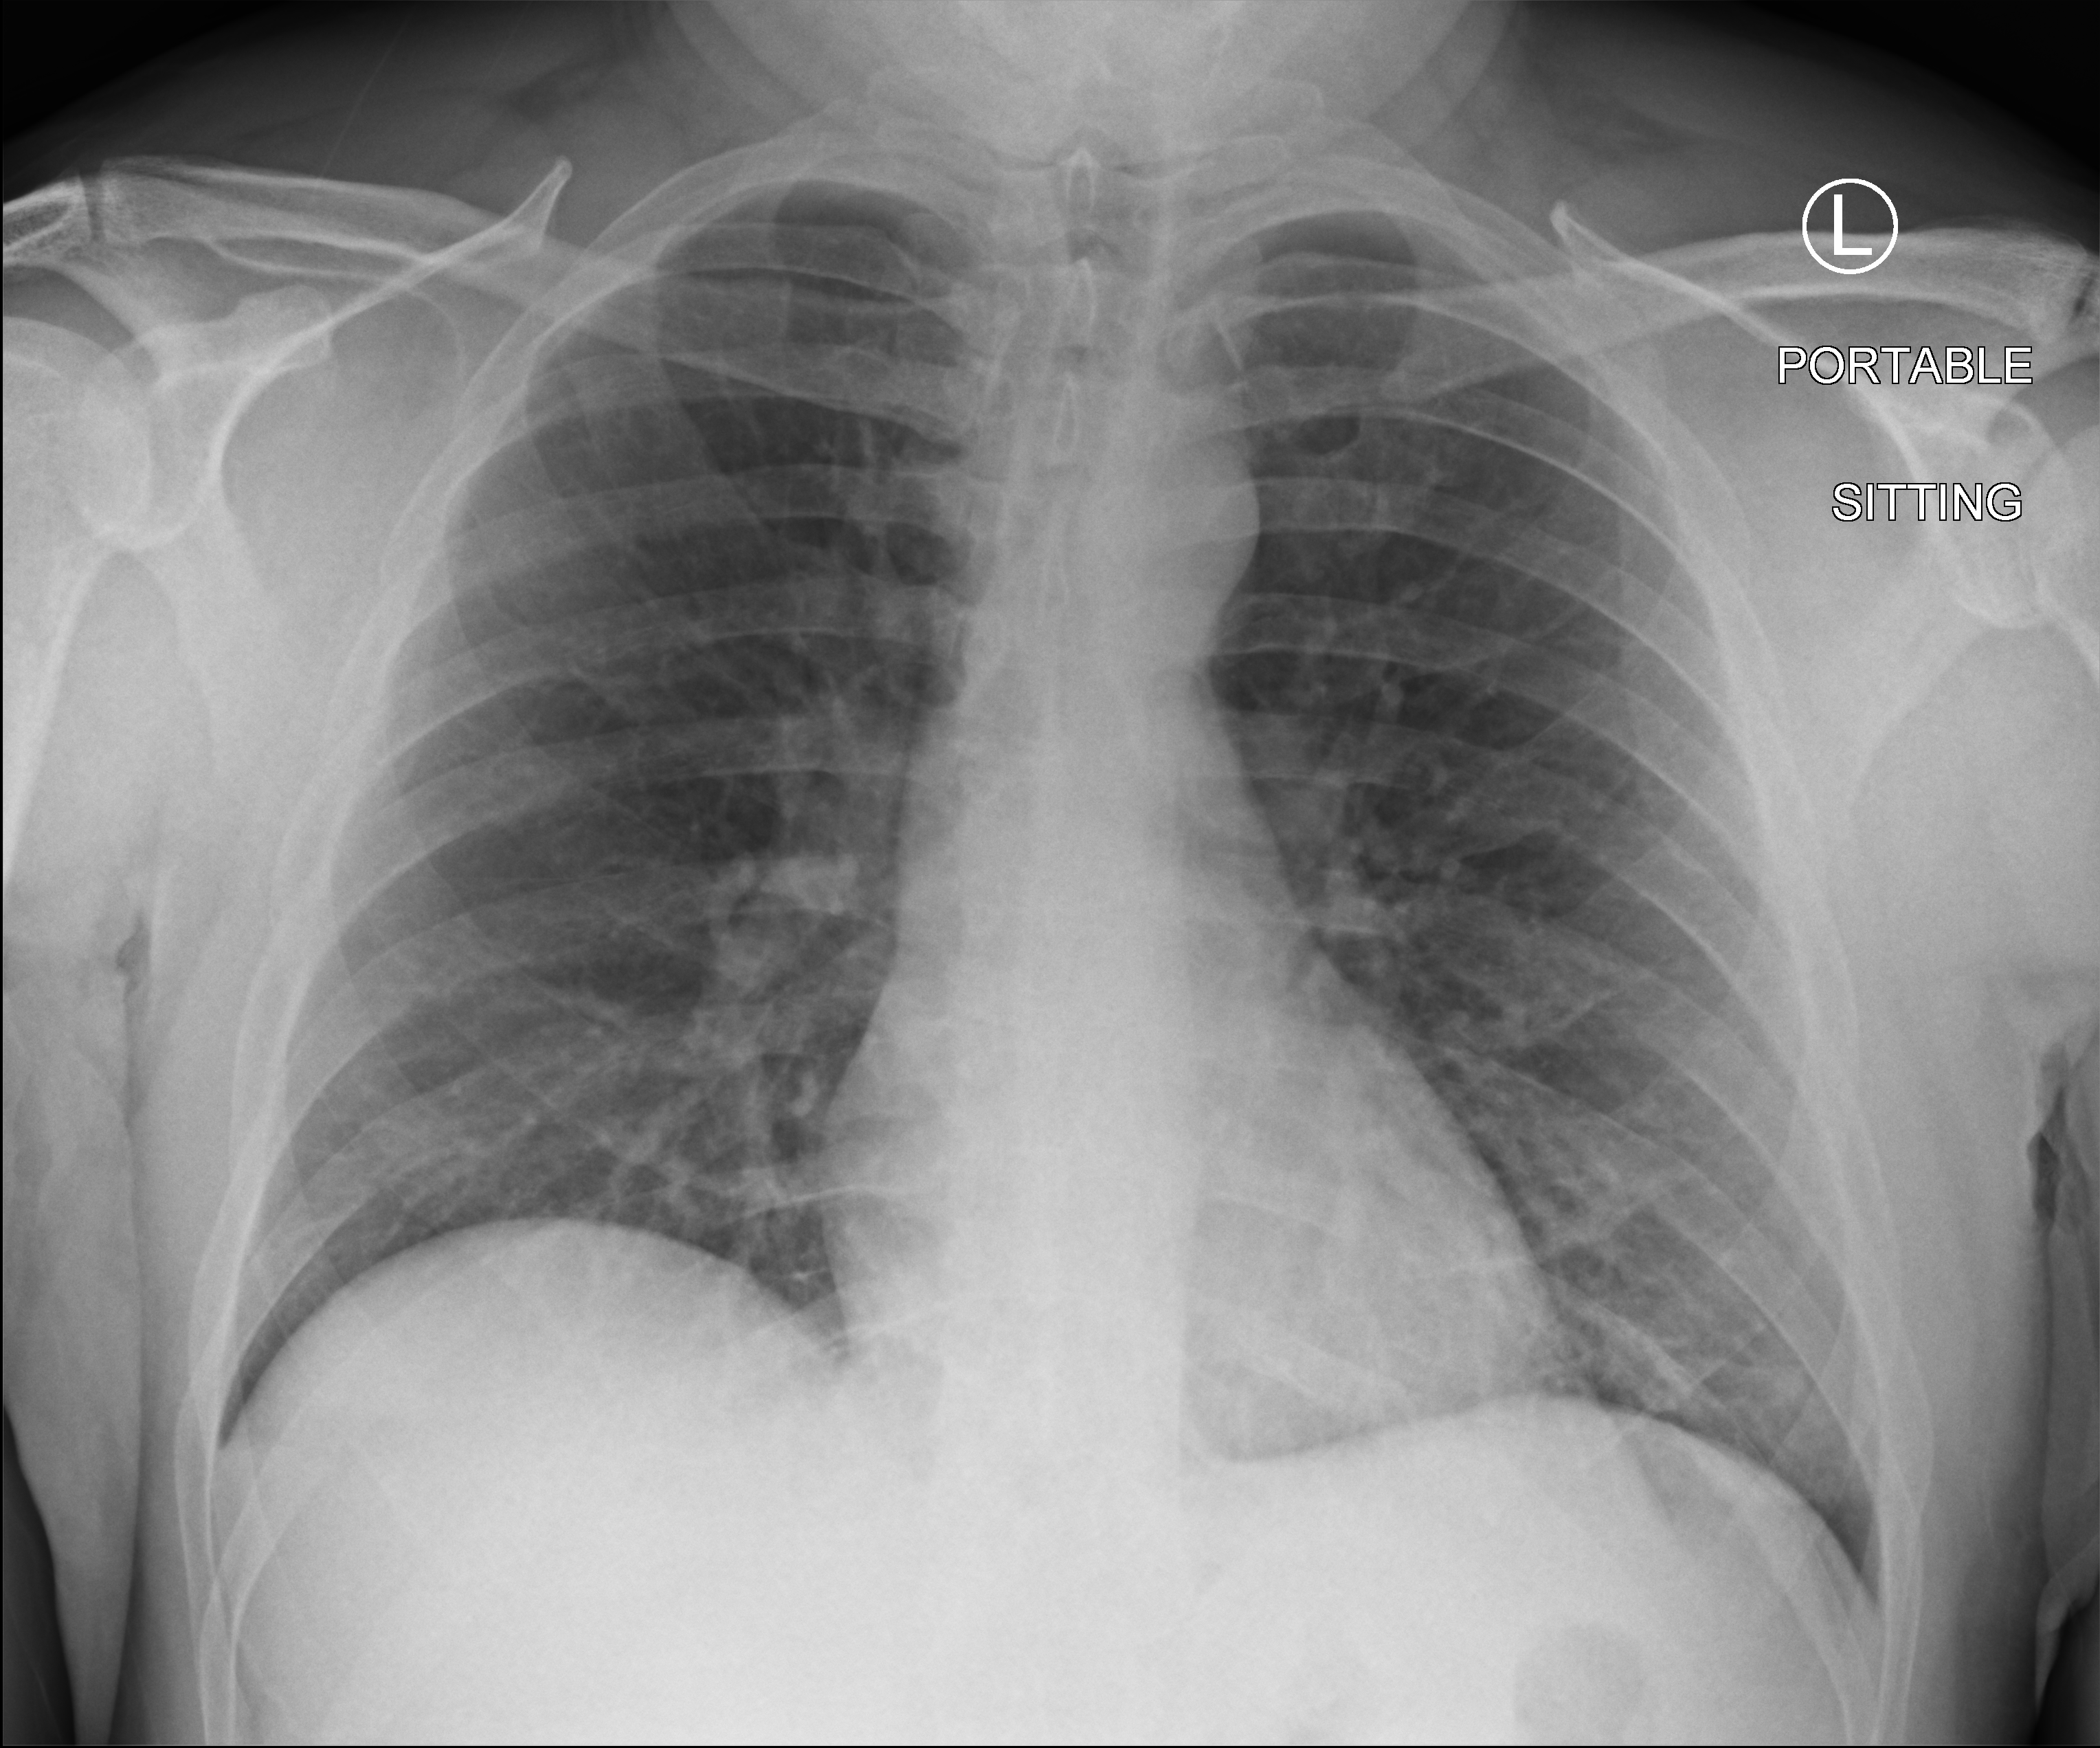
Bedside chest radiograph (computed radiography), anteroposterior (AP) projection. Patient hospitalised with COVID-19; male, aged 18–59 years.
Admission-level facts for this patient (not findings on this image; timing relative to this image not recorded):
- mechanically ventilated during this hospital stay: no
- admitted to intensive care during this hospital stay: no